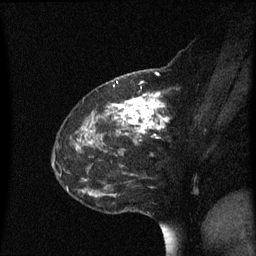
Breast MRI (dynamic contrast-enhanced), one sagittal slice; slice 22 of 60 in the series (ordered by position); dynamic contrast-enhanced series, image 2 of 3 at this slice position (ordered by acquisition); 1.5 T; TE 4.2 ms, TR 8.4 ms; 256 × 256 image matrix. Female patient, age 48 years. From the clinical record (not read from this slice): setting: breast cancer imaged before/during neoadjuvant chemotherapy; receptor status: HR-positive, HER2-negative.
Structures marked on this image (semi-automatic segmentation, software-assisted and operator-edited):
- analysis volume of interest (the breast-tissue region the enhancement analysis was run in; not a lesion): bounding box <80,78,195,217> (left, top, right, bottom; pixels)
- tumour enhancement mask (voxels above the 70 % enhancement threshold inside the analysis volume of interest): <80,82,169,144>